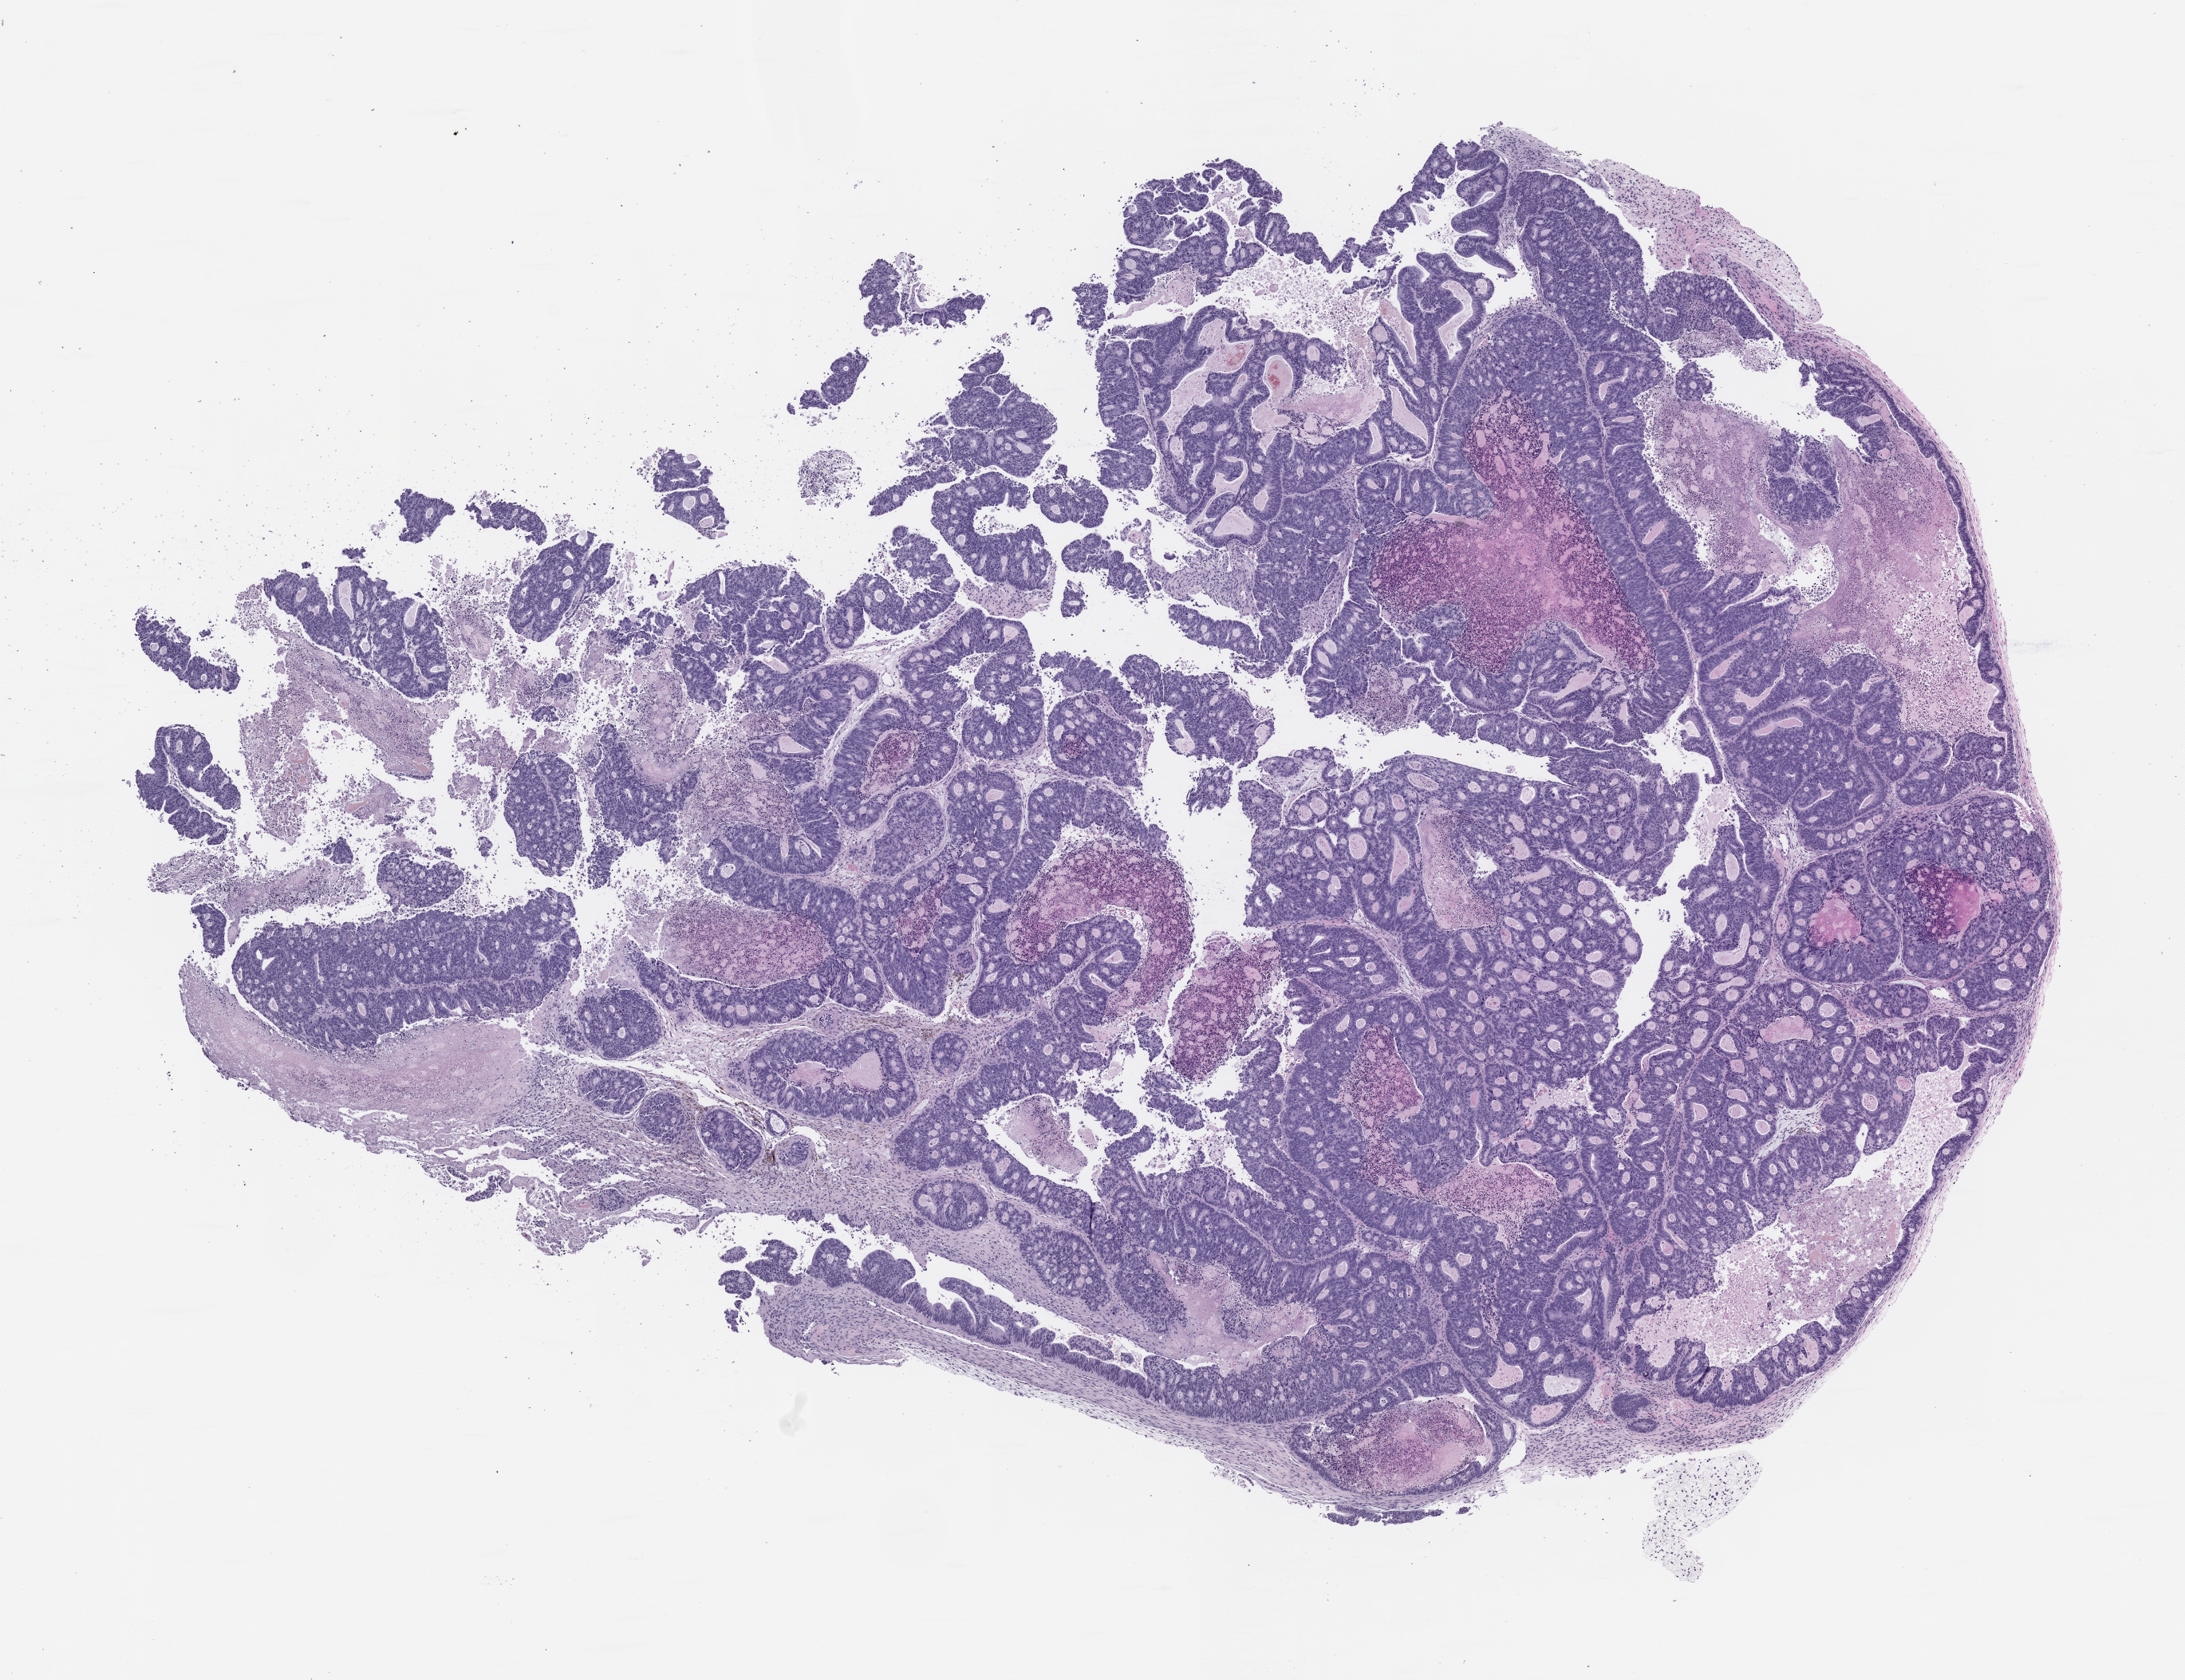
Whole-slide image, H&E: patient-derived xenograft (human tumor grown in a mouse), passage 1, shown as a low-resolution overview of the whole scanned area (about 11.0 x 8.5 mm), formalin-fixed paraffin-embedded section, tumor site category: colon.
Originating patient diagnosis: Colon Adenocarcinoma.